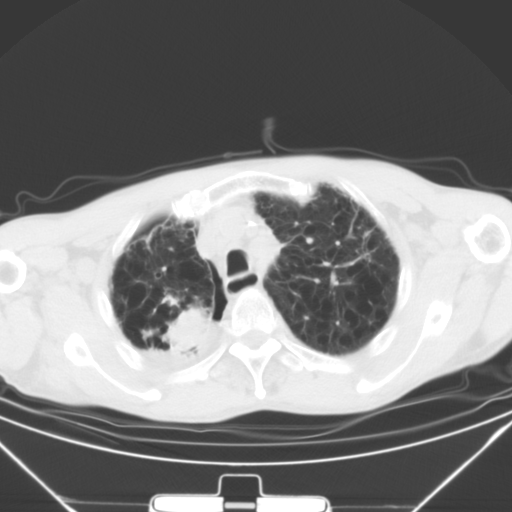
Chest CT, one axial slice. 120 kVp. Lung window (W 1500 / L -600 HU). 512 × 512 image matrix. Patient: male, 65 years. Case-level facts recorded for this patient, not image findings: clinical TNM (as recorded): T3 N1 M1a.
Structures marked on this image (rectangle marked by the reading radiologist):
- lung tumour (recorded histology: squamous cell carcinoma): bounding box (x1, y1, x2, y2) in pixels: (166, 302, 215, 359)